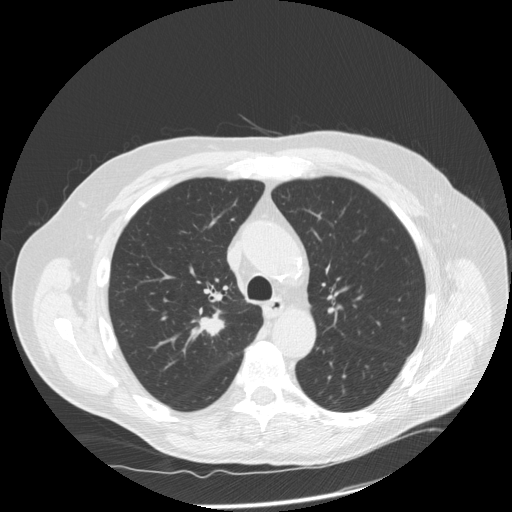
Chest CT (low-dose screening protocol), one axial image, third screening round (two years after baseline), lung window (W 1500 / L -600 HU), standard (soft-tissue) reconstruction kernel (STANDARD), 120 kVp, slice 52 of 166 in the series. Male participant, aged 69 years at enrolment. Former smoker at enrolment.
Expert reader's lesion annotation, box from (x=184, y=299) to (x=242, y=349) px. Screening reader's record for this exam (one nodule recorded; not confirmed to be the boxed lesion): non-calcified nodule or mass ≥4 mm, right upper lobe, 18 × 17 mm, spiculated (stellate) margins, soft tissue attenuation, pre-existing on the prior screen: no. Official screen result: positive, other. Lung cancer was diagnosed 13 days after this screen: squamous cell carcinoma, NOS, right upper lobe, poorly differentiated (G3), stage IA (AJCC 6th edition), 22 mm at pathology.